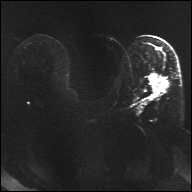
Breast MRI, one axial slice; slice 17 of 32 in the series (ordered by position); diffusion-weighted series; image 2 of 4 stored at this slice position (different b-values; order by instance number); 1.5 T; 4 mm slice thickness; 192 × 192 image matrix. Female patient.
Structures marked on this image (expert manual segmentation):
- tumour on diffusion-weighted imaging: bounding box (x1, y1, x2, y2) in pixels: (149, 76, 169, 94)